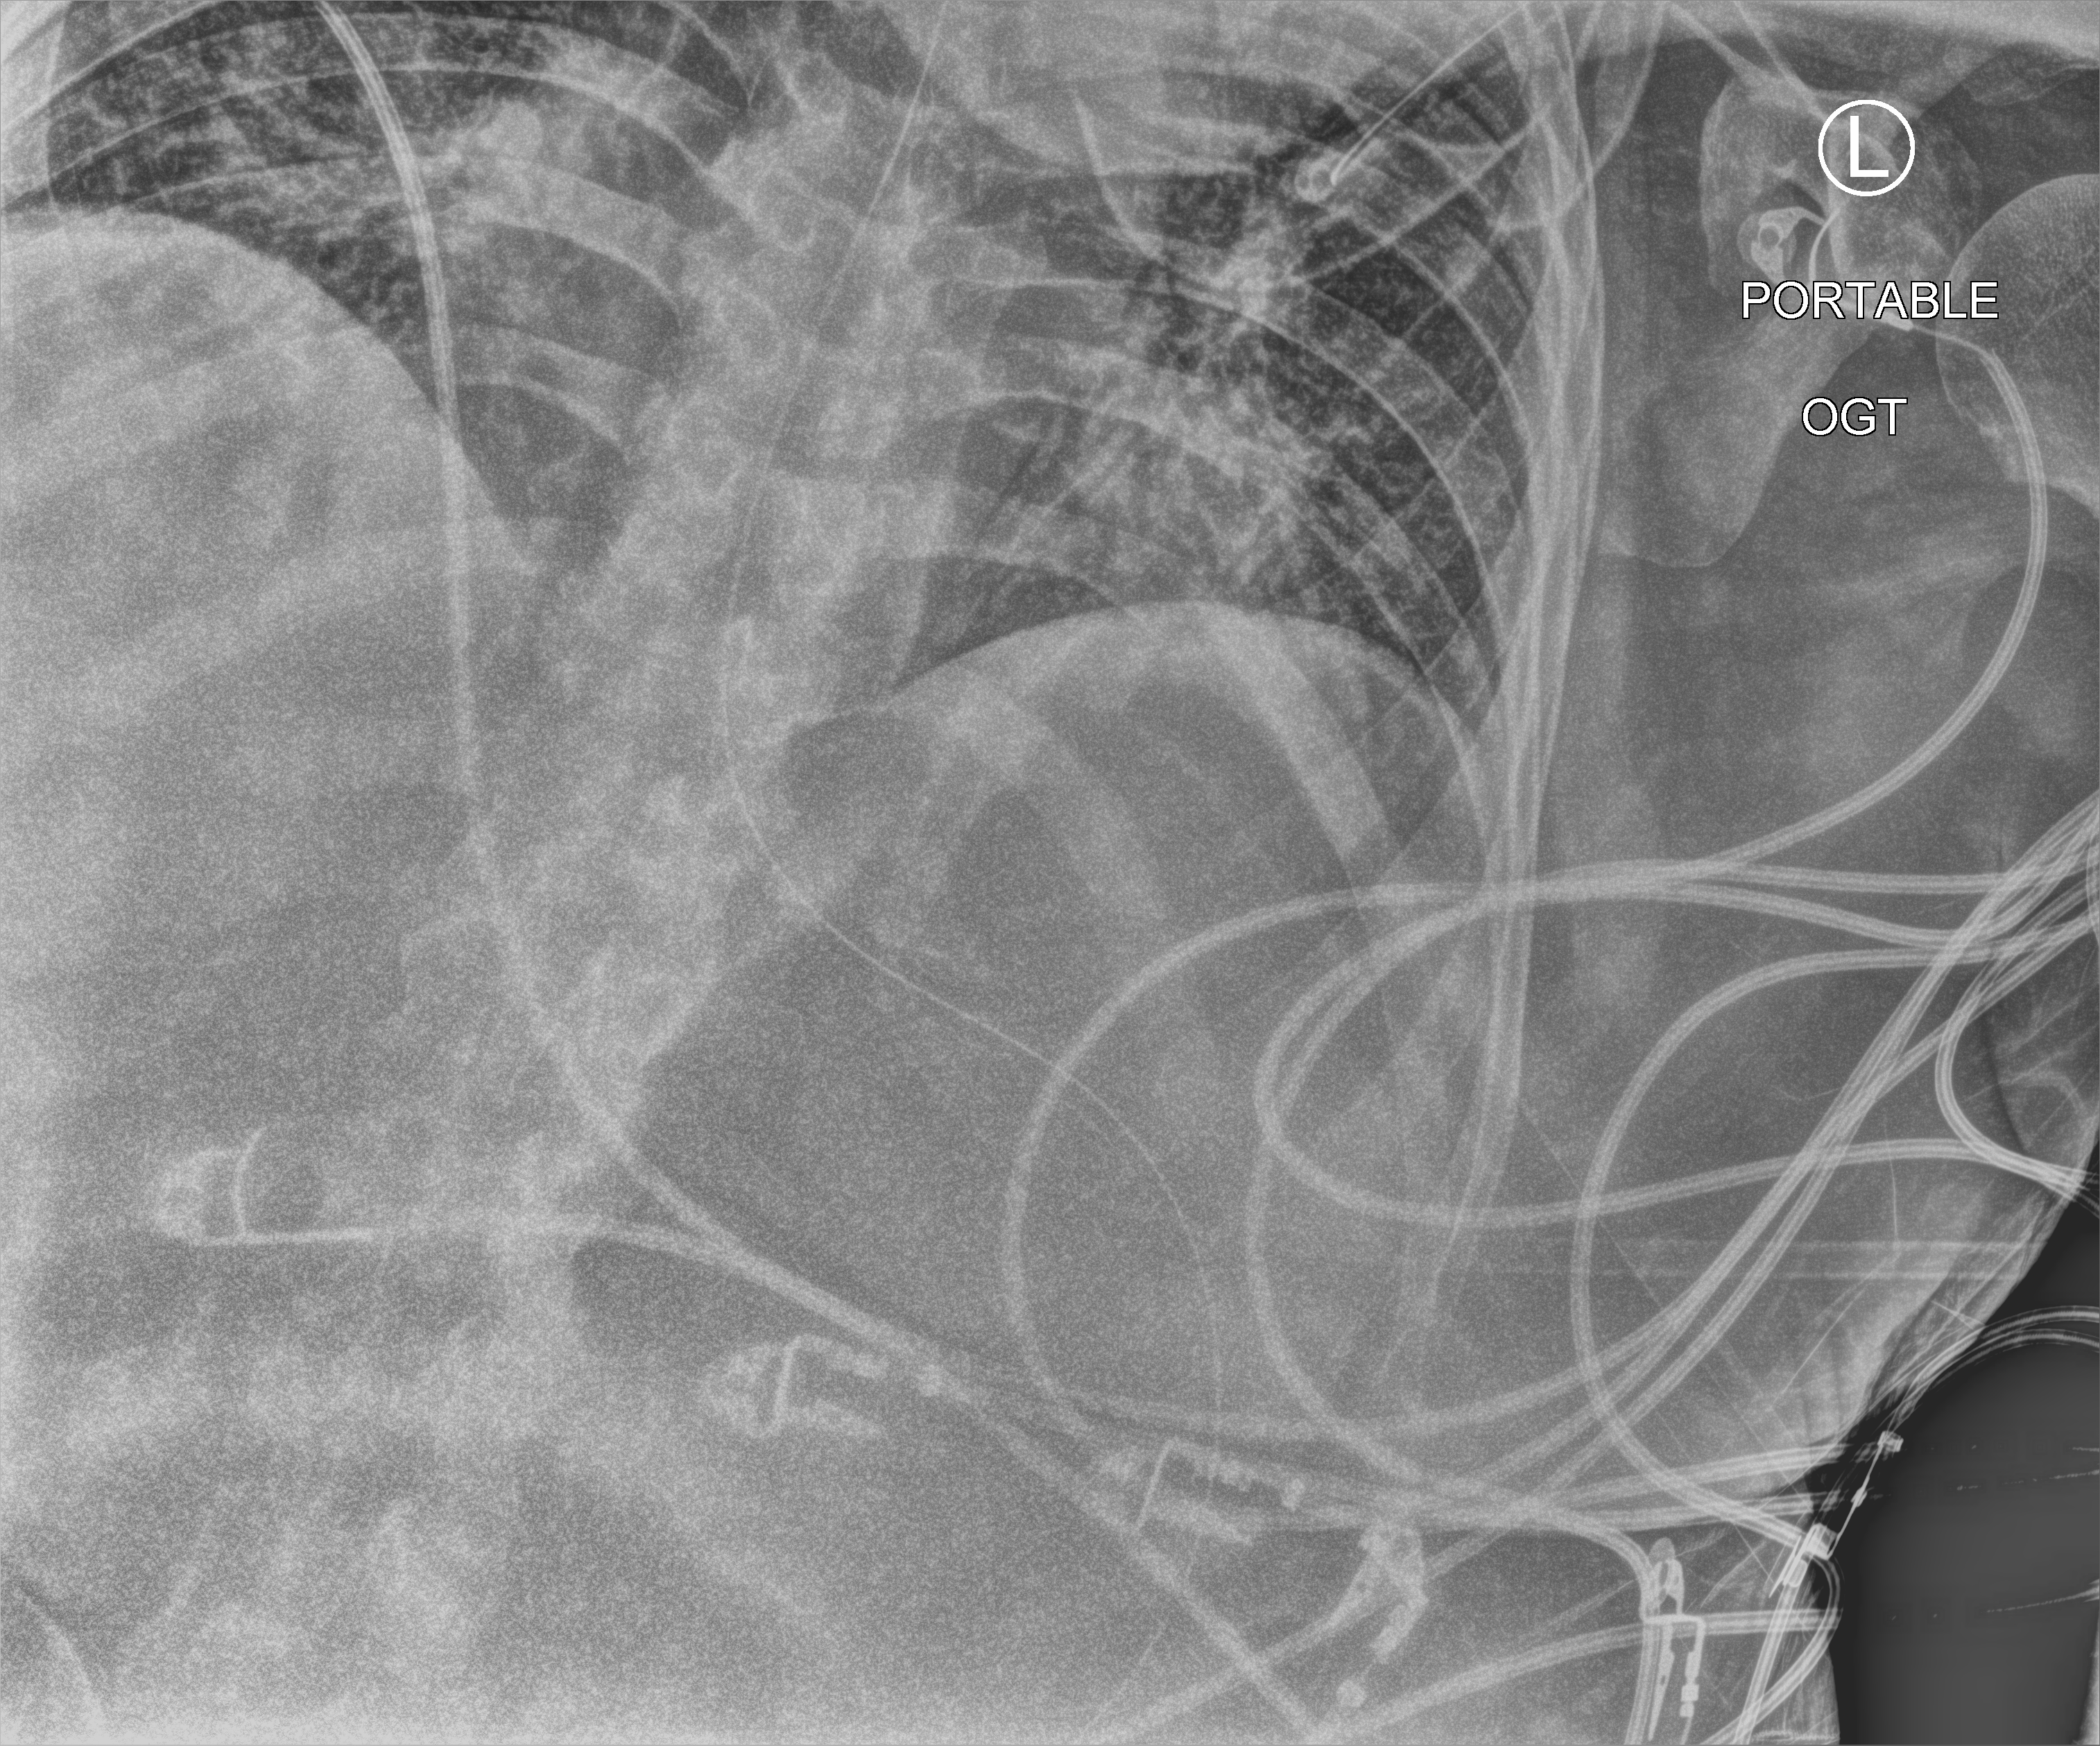
Portable chest radiograph. Patient hospitalised with COVID-19; male, aged 18–59 years.
Hospital-stay facts (about this admission, not read from this image; timing relative to this image not recorded): admitted to intensive care during this hospital stay: yes; length of hospital stay: 28 days.